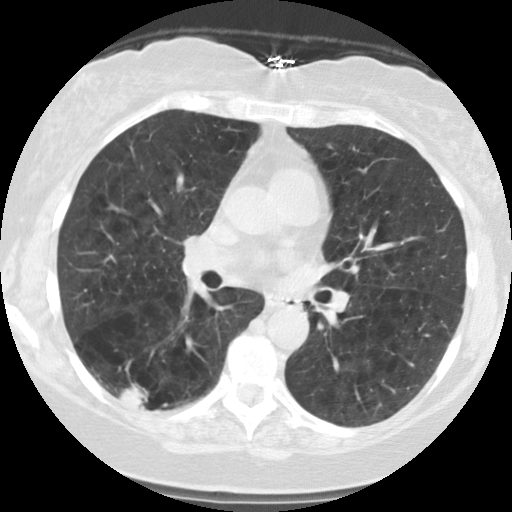
Chest CT (low-dose screening protocol), one axial image. Second screening round (one year after baseline). Lung window (W 1500 / L -600 HU). 140 kVp. Slice 61 of 122 in the series. 512 × 512 image matrix, field of view 310 × 310 mm. Female, age 59 years at enrolment.
Expert reader's lesion annotation, box from (x=106, y=362) to (x=181, y=424) px. The screening reader recorded 2 non-calcified nodules or masses ≥4 mm on this exam; which of them this box marks is not recorded. Official screen result: positive, other. Lung cancer was diagnosed 63 days after this screen: squamous cell carcinoma, NOS, right lower lobe, poorly differentiated (G3), stage IB (AJCC 6th edition), 30 mm at pathology.